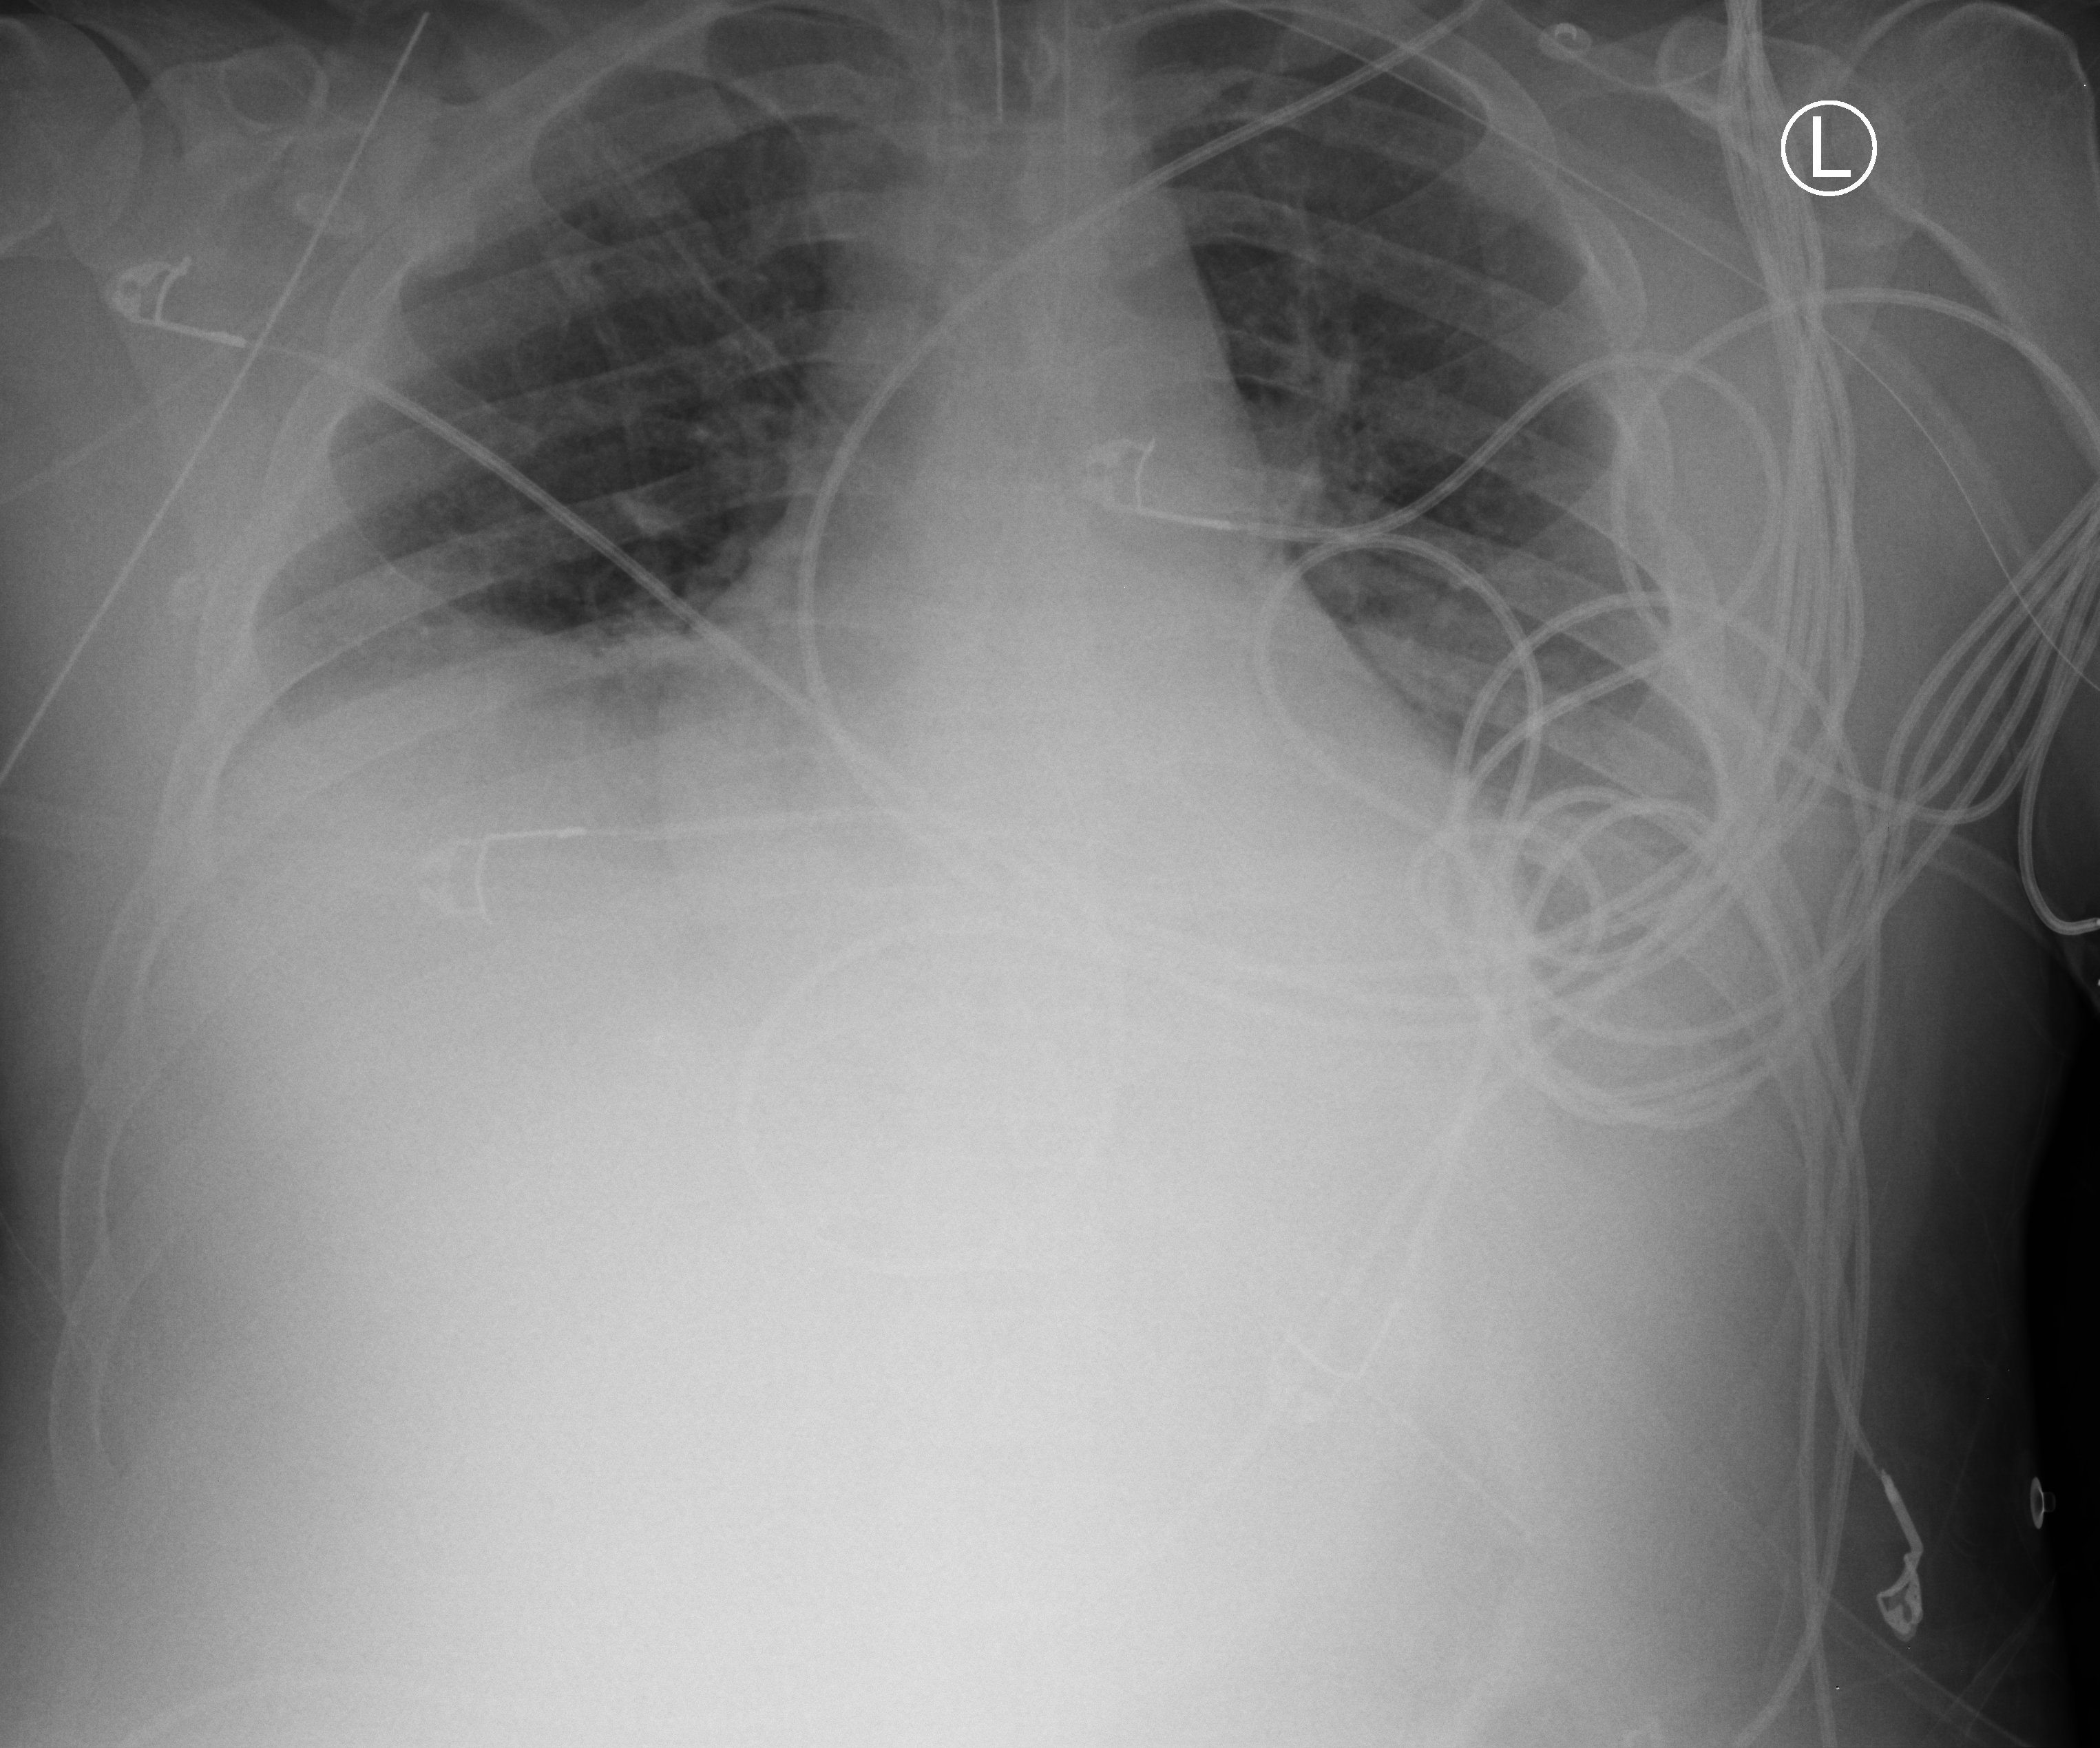
Chest X-ray (portable); anteroposterior (AP) projection. Male patient hospitalised with COVID-19, age 18–59 years.
From the hospital-stay record, not from the radiograph (when in the stay this image was taken is not recorded): mechanically ventilated during this hospital stay: yes.